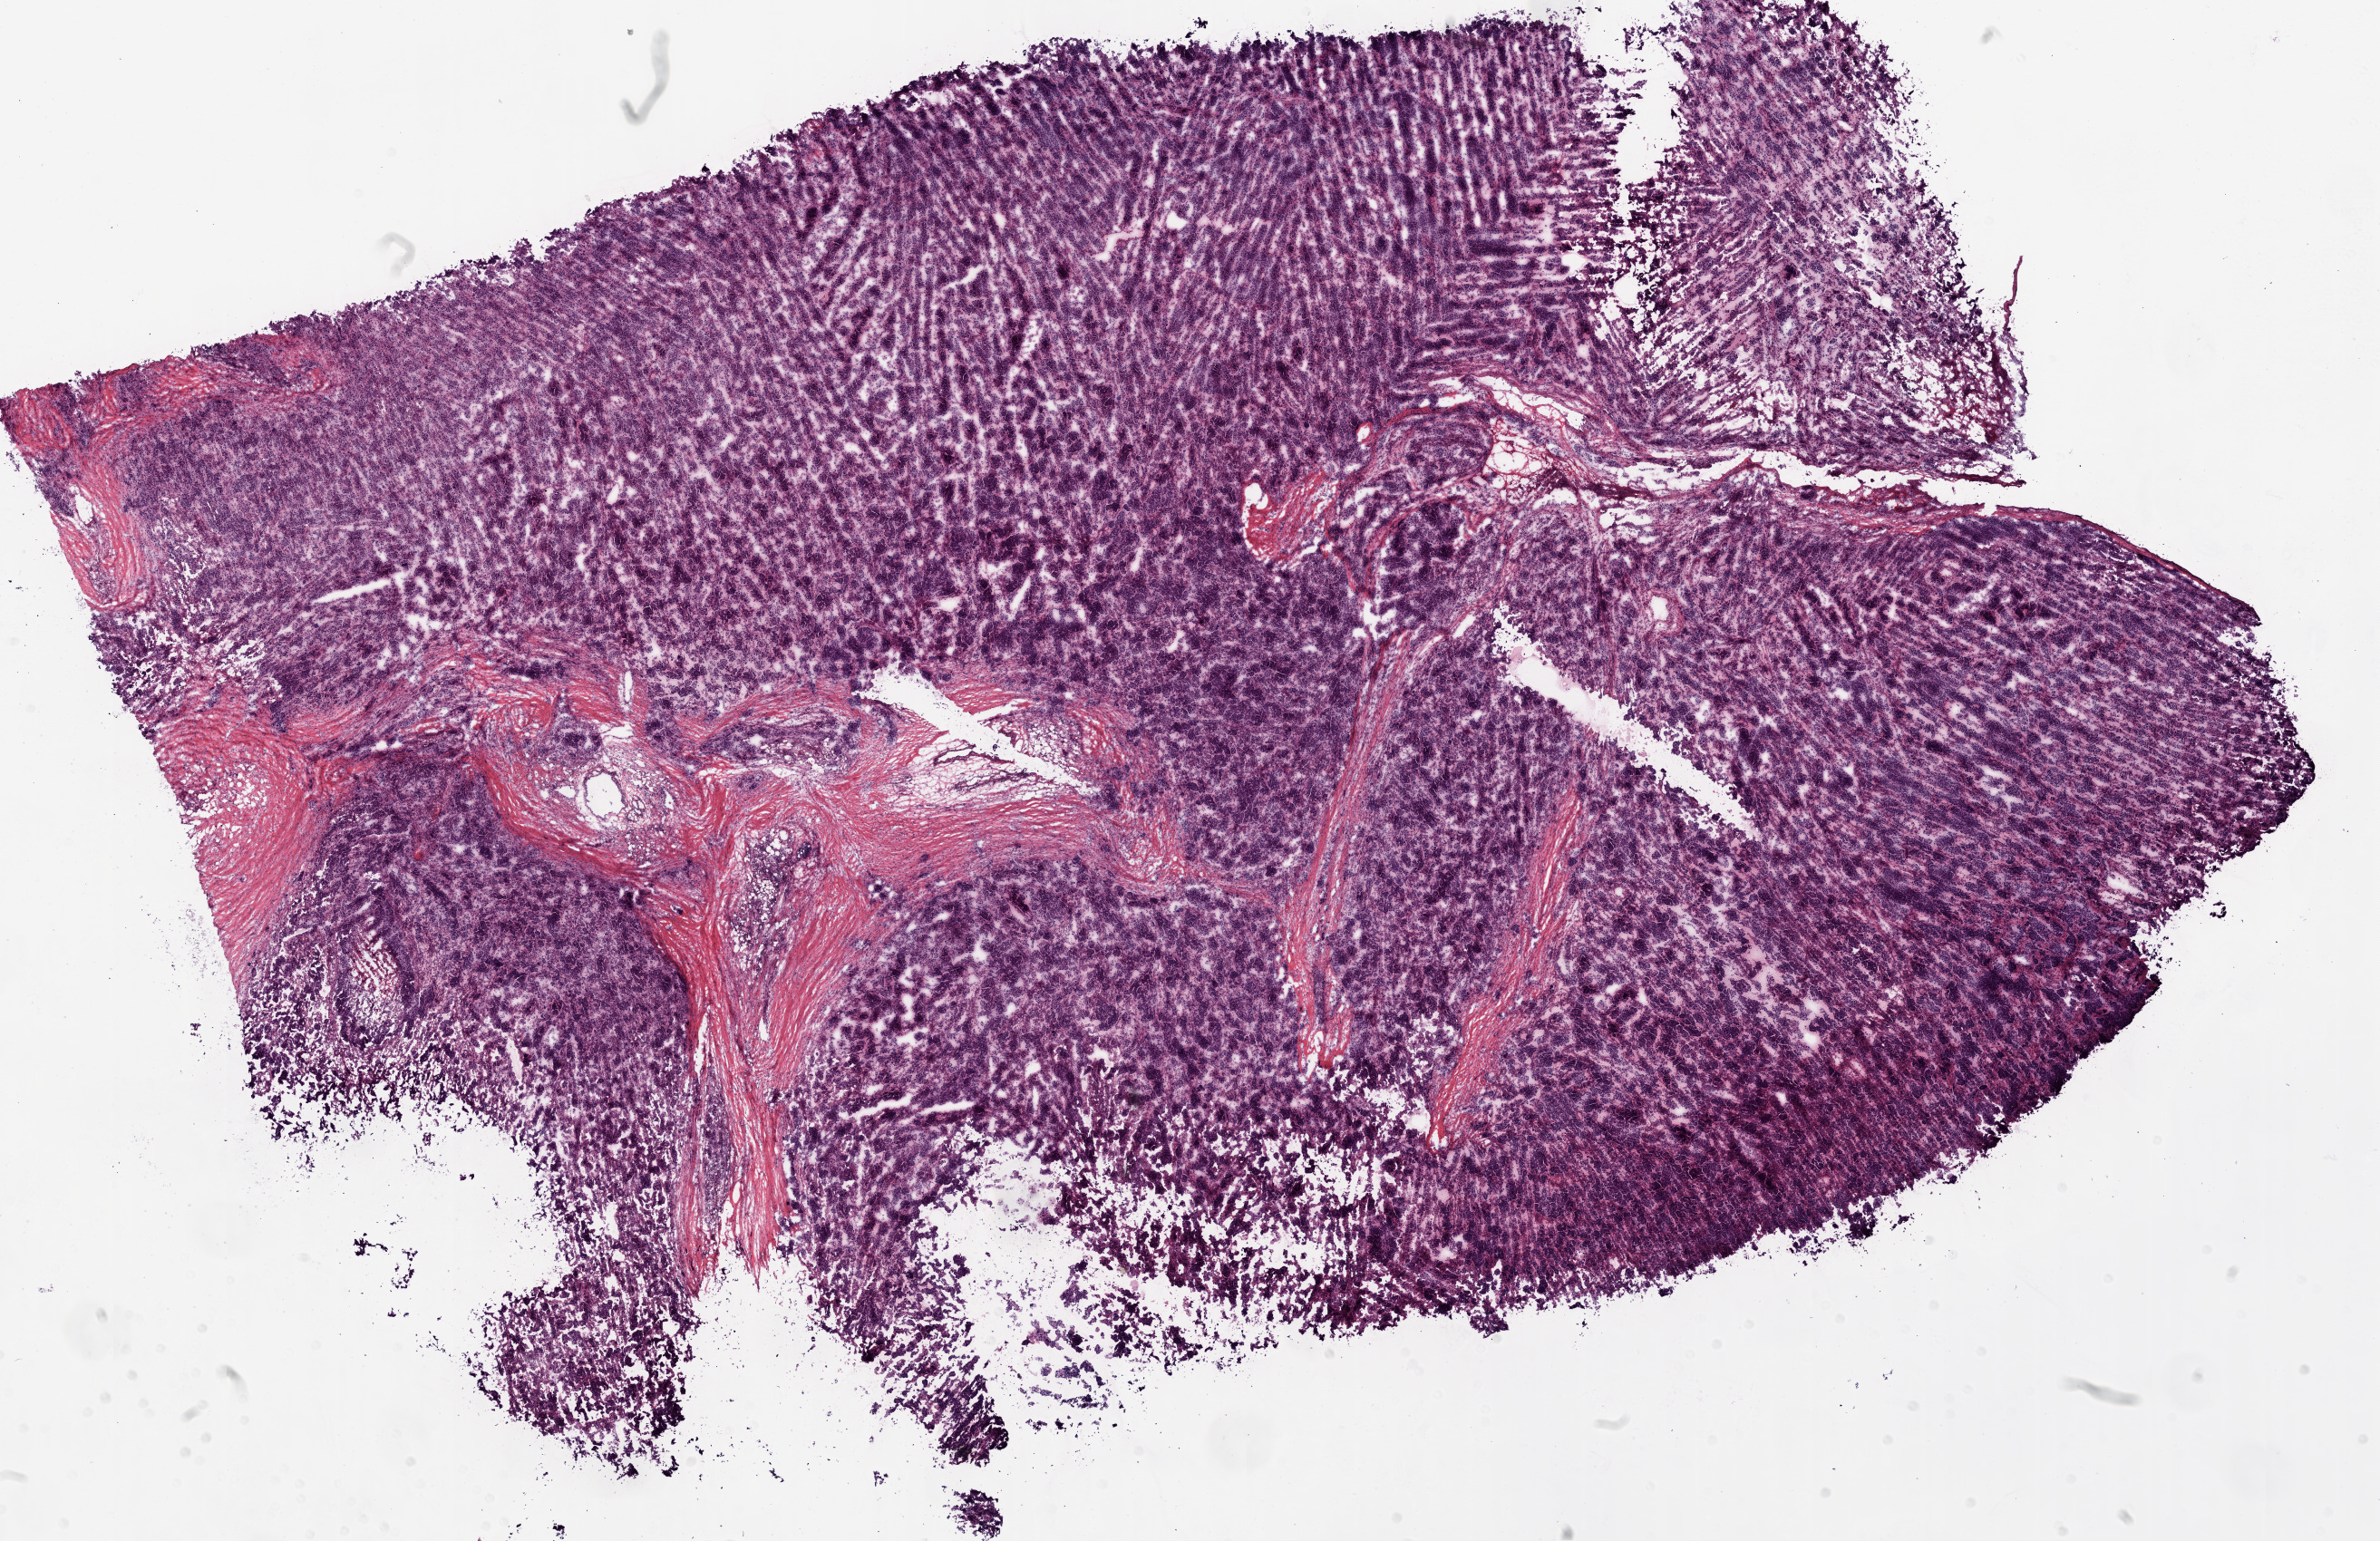
Digitized H&E tissue section (whole slide) — low-resolution overview of the scanned area, about 21.1 x 13.6 mm (from a 20x scan). Frozen section from the top of the tissue portion. Ovary, primary tumour sample. Female patient; age at initial diagnosis 68 years. Histologic grade: G3 (poorly differentiated). Slide review estimates, as recorded: tumour cells 94%, tumour nuclei 95%, normal cells 0%, stromal cells 5%, necrosis 1%.
FIGO stage: IIIC. Pathologic diagnosis: Serous cystadenocarcinoma, NOS.